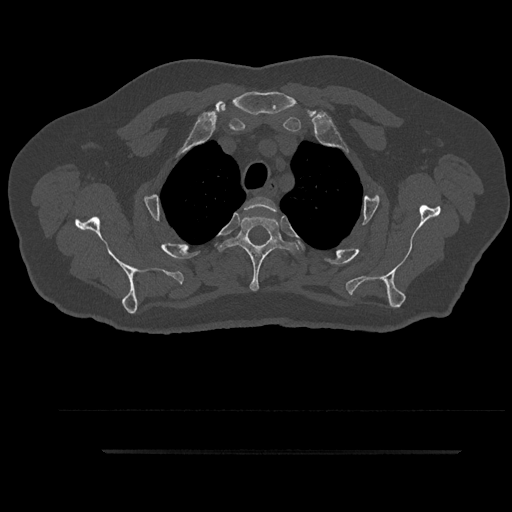
CT including the spine, one axial slice; slice 721 of 797 in the series (ordered by position); reconstruction kernel Br40s/3; bone window (W 1800 / L 400 HU); 0.5 mm slice thickness; 512 × 512 image matrix, field of view 432 × 432 mm. Male patient, age 63 years. From the clinical record (not read from this slice): primary cancer: renal; vertebrae with lytic lesions (as recorded): T8.
Structures marked on this image (semi-automatically segmented with operator editing):
- T2 vertebra: box from (x=245, y=197) to (x=277, y=212) px
- T3 vertebra: (x=219, y=215)–(x=299, y=291)